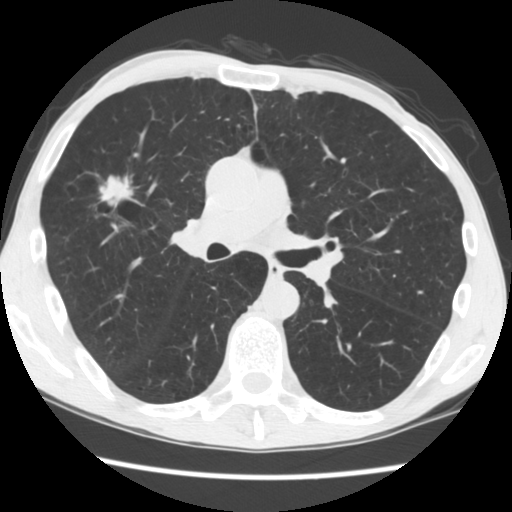
Low-dose screening chest CT, one axial slice; position 101 of 181 along the scan axis; 120 kVp; lung window (W 1500 / L -600 HU); 2.5 mm slice thickness; 512 × 512 image matrix, field of view 330 × 330 mm.
Annotated regions visible in this slice (expert manual segmentation):
- lesion 1 (tumor, upper lobe of right lung): bounding box [x1, y1, x2, y2] px = [99, 175, 134, 208]